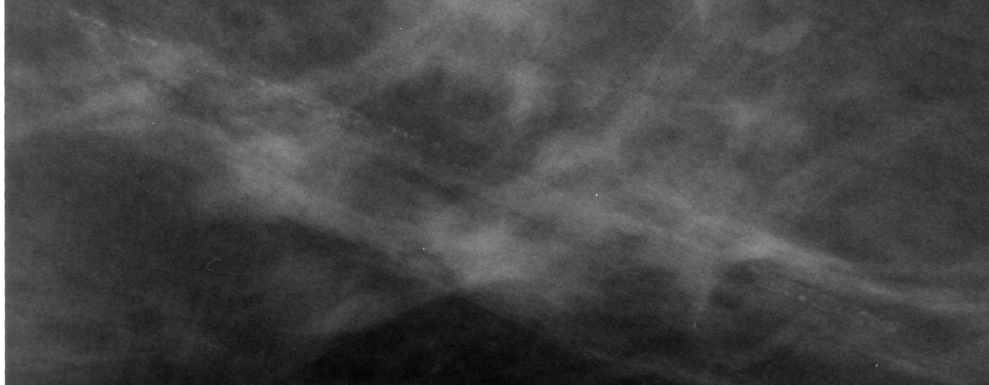
Region of interest cut from a scanned film mammogram (one marked finding); left breast; CC view.
- Calcifications, morphology vascular; BI-RADS assessment category 2; subtlety rating 4 on a 1 (subtle) to 5 (obvious) scale; benign without callback (not worked up further).